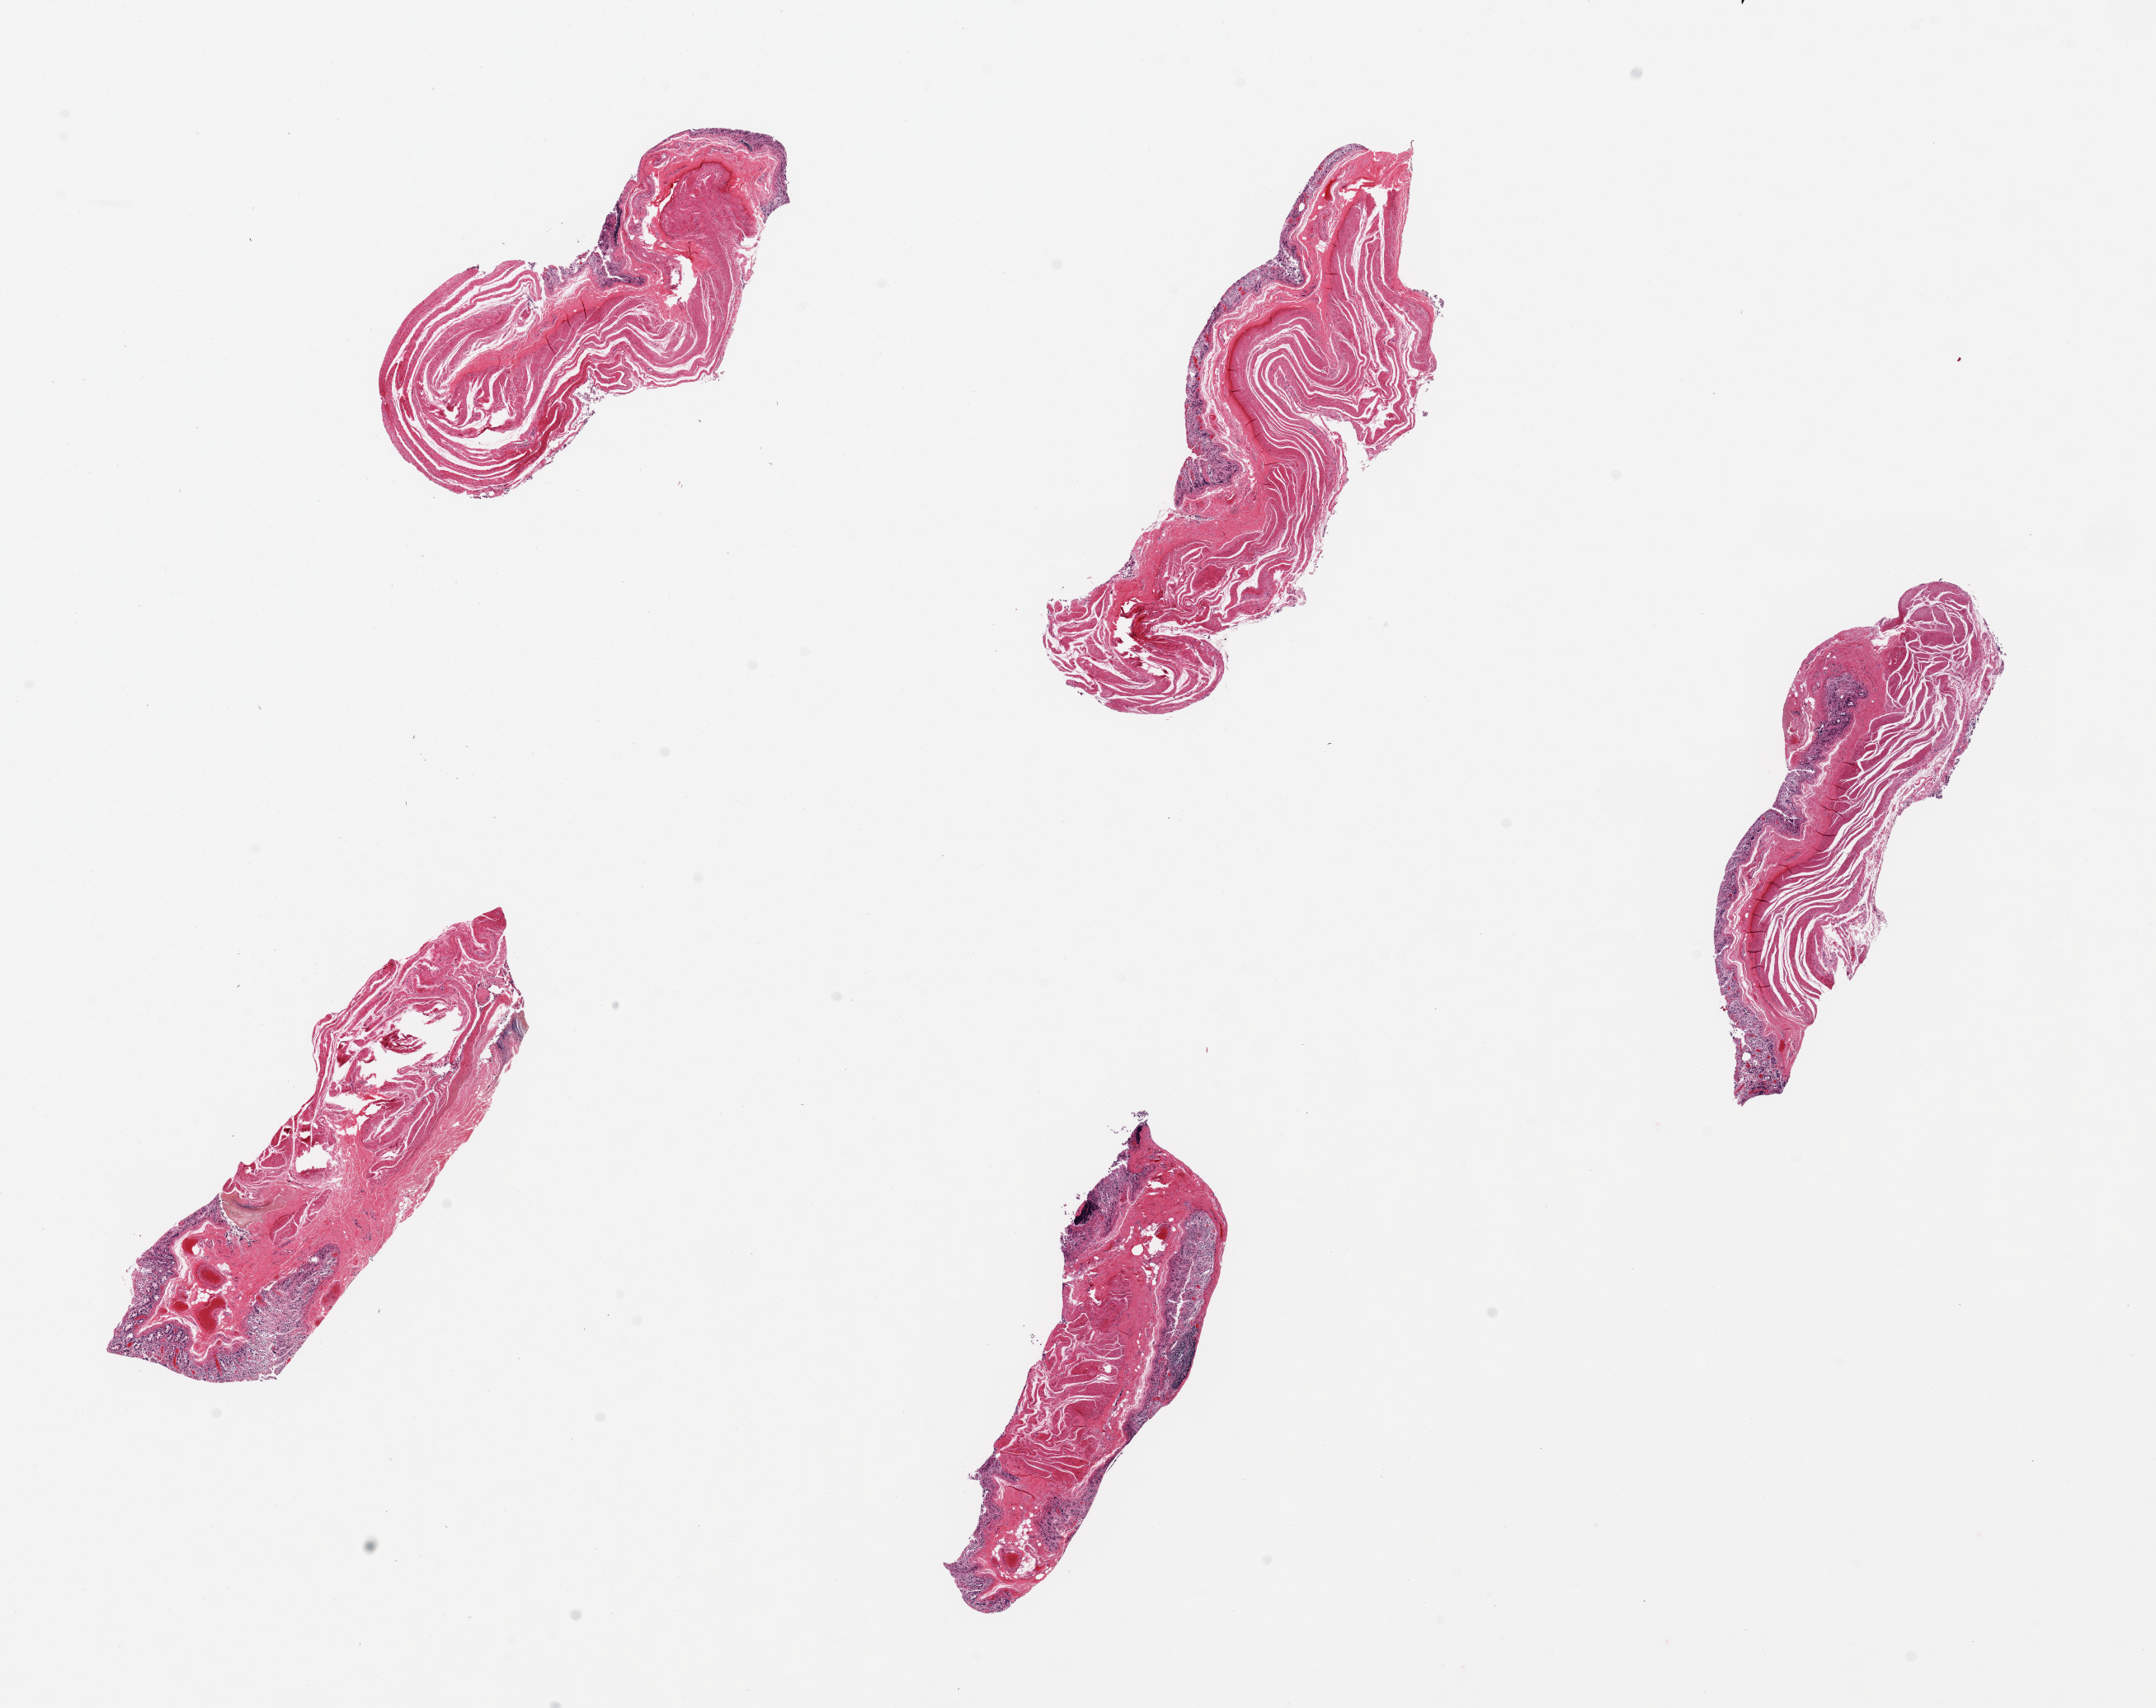
Haematoxylin and eosin whole-slide image, brightfield — low-resolution overview of the scanned area, about 20.7 x 16.4 mm, PAXgene-fixed, paraffin-embedded tissue, target tissue: ileum, donor tissue sample. Donor: male.
Pathologist's review note for this sample: 5 pieces, up to 6x2mm; 2 lymphoid nodules; autolyzed mucosa; all have (UNWANTED muscularis).